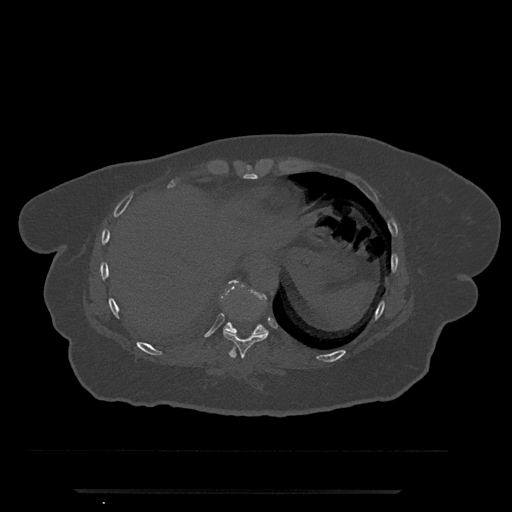
CT including the spine, one axial slice; position 321 of 797 along the scan axis; reconstruction kernel Br40s/3; 120 kVp; bone window (W 1800 / L 400 HU); 512 × 512 image matrix, field of view 440 × 440 mm. Female patient, age 51 years. Case-level facts recorded for this patient, not image findings: primary cancer: neuro.
Structures marked on this image (semi-automatic segmentation, software-assisted and operator-edited):
- T10 vertebra: bounding box <223,280,267,336> (left, top, right, bottom; pixels)
- T9 vertebra: <223,331,269,359>